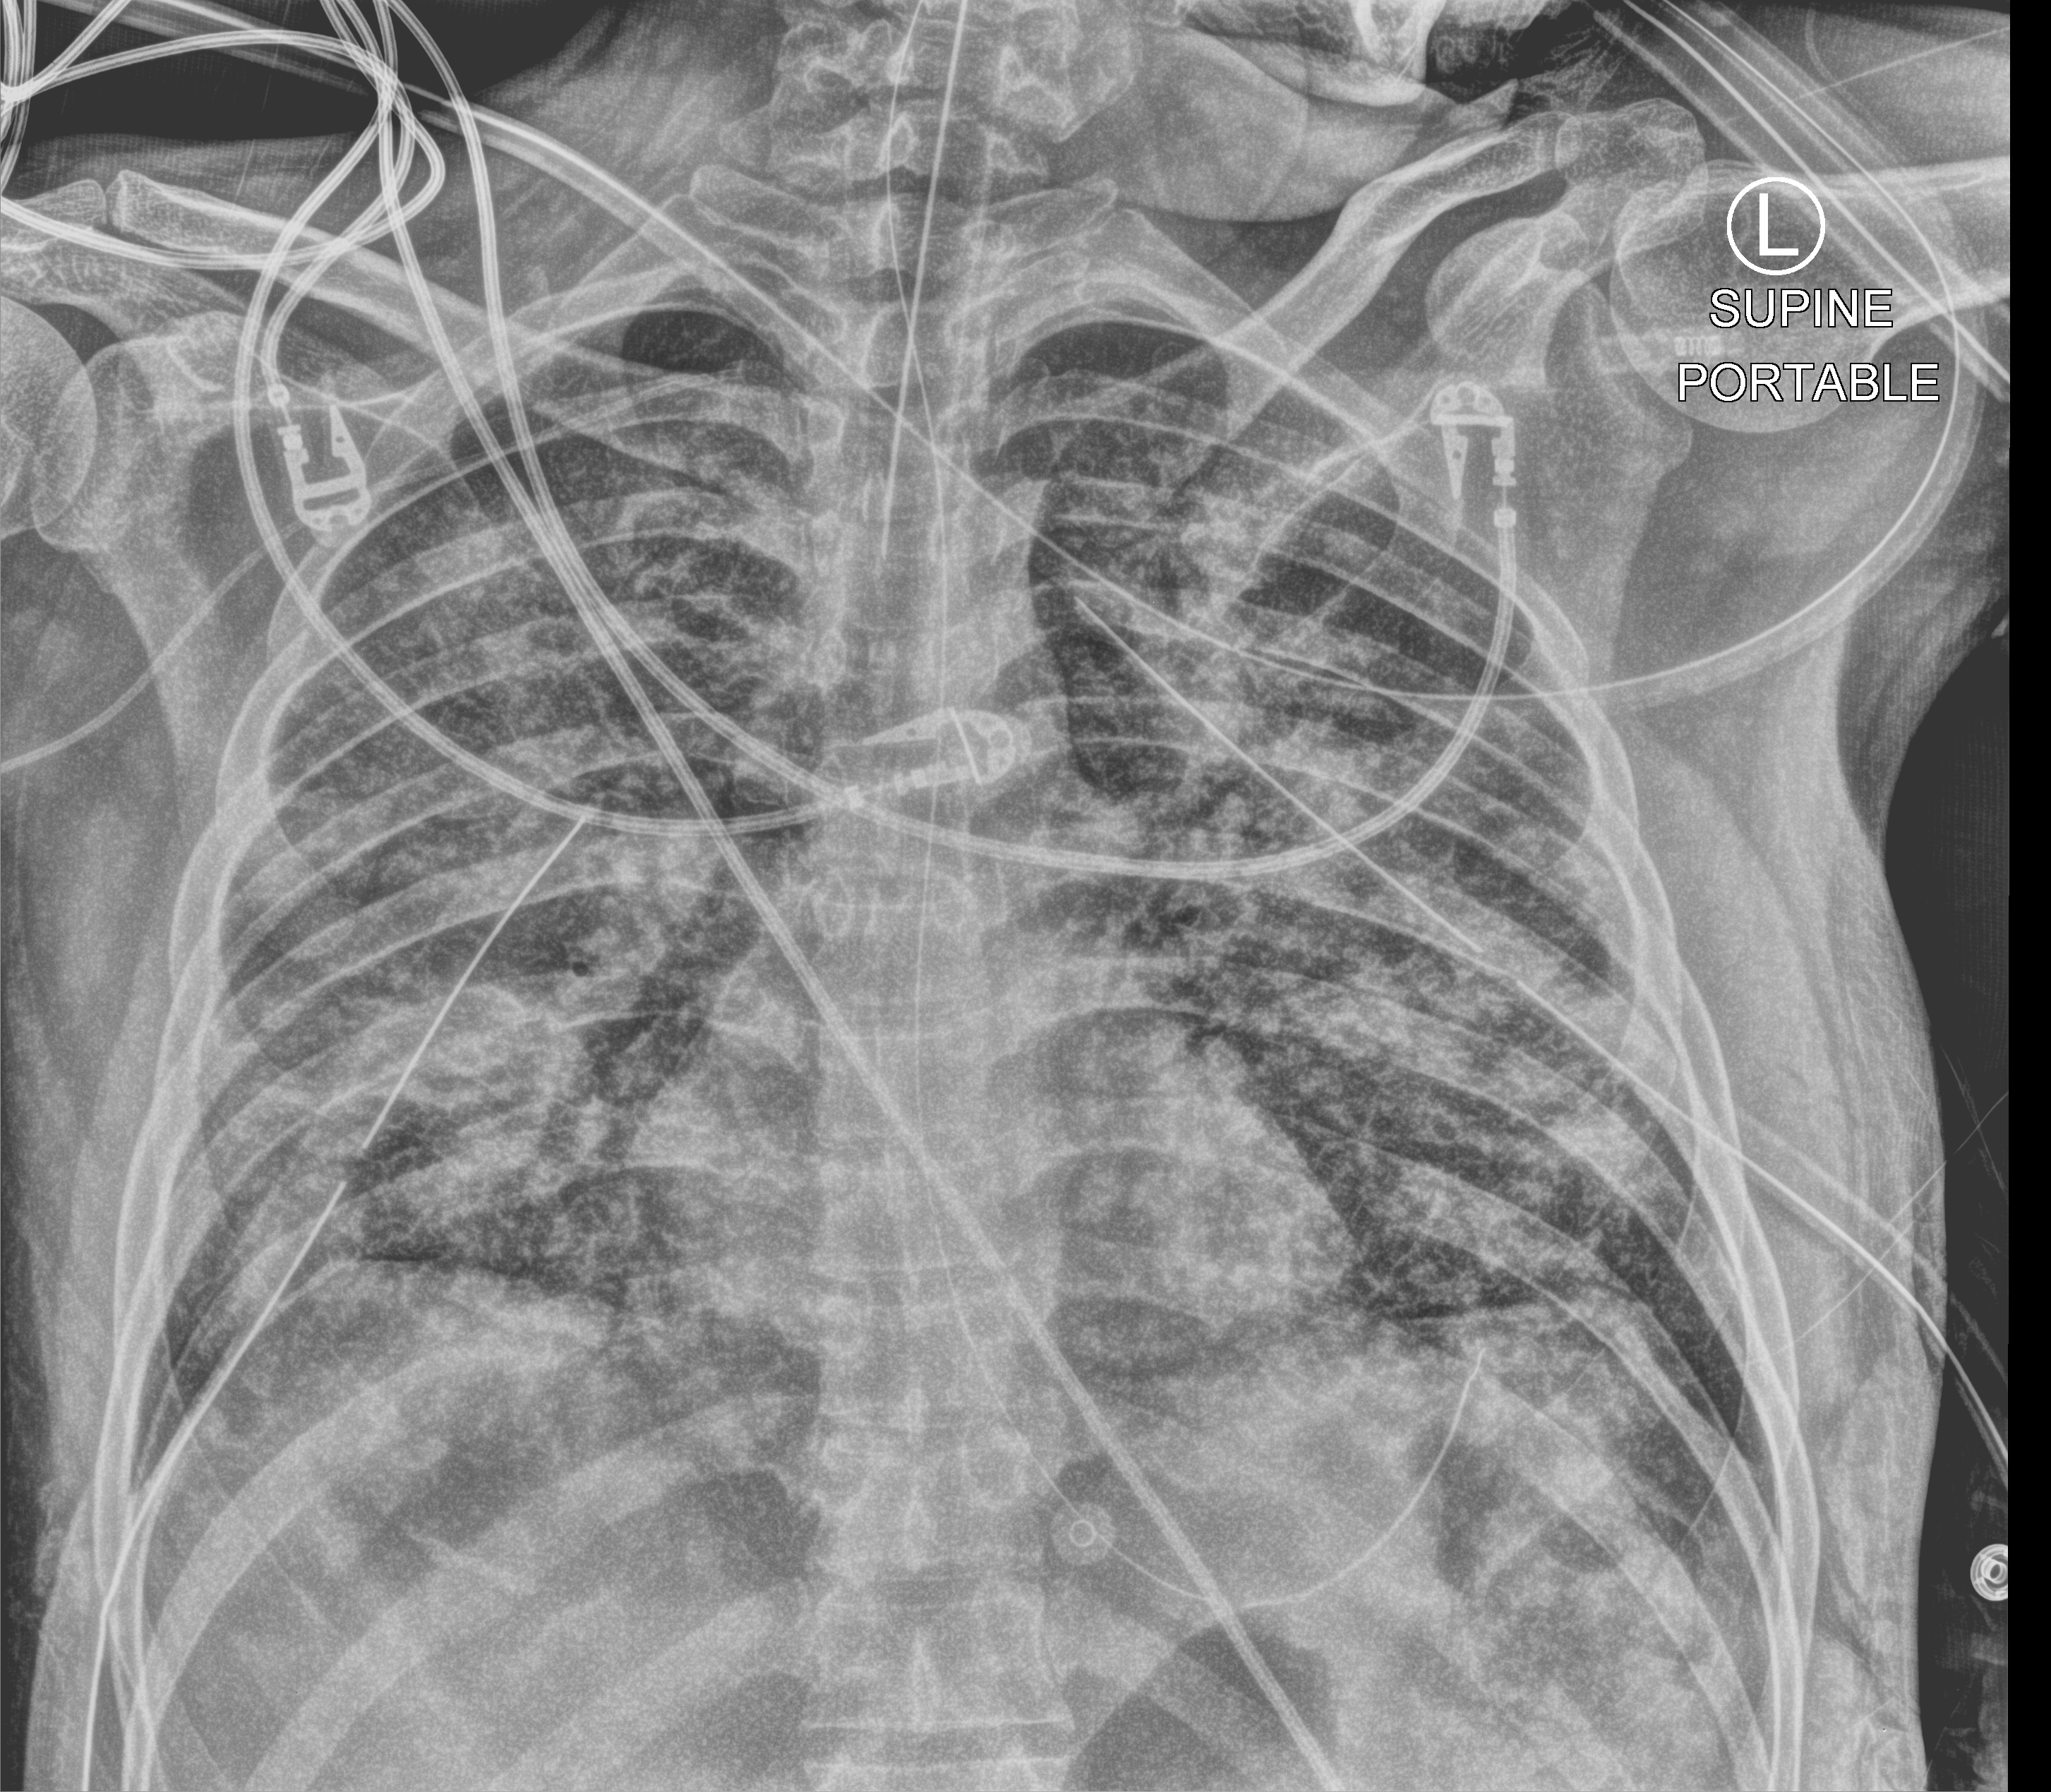
Portable chest radiograph, anteroposterior (AP) projection. Patient hospitalised with COVID-19; male, aged 18–59 years.
Admission-level facts for this patient (not findings on this image; timing relative to this image not recorded): mechanically ventilated during this hospital stay: yes; COPD (admission record): no; length of hospital stay: 29 days.